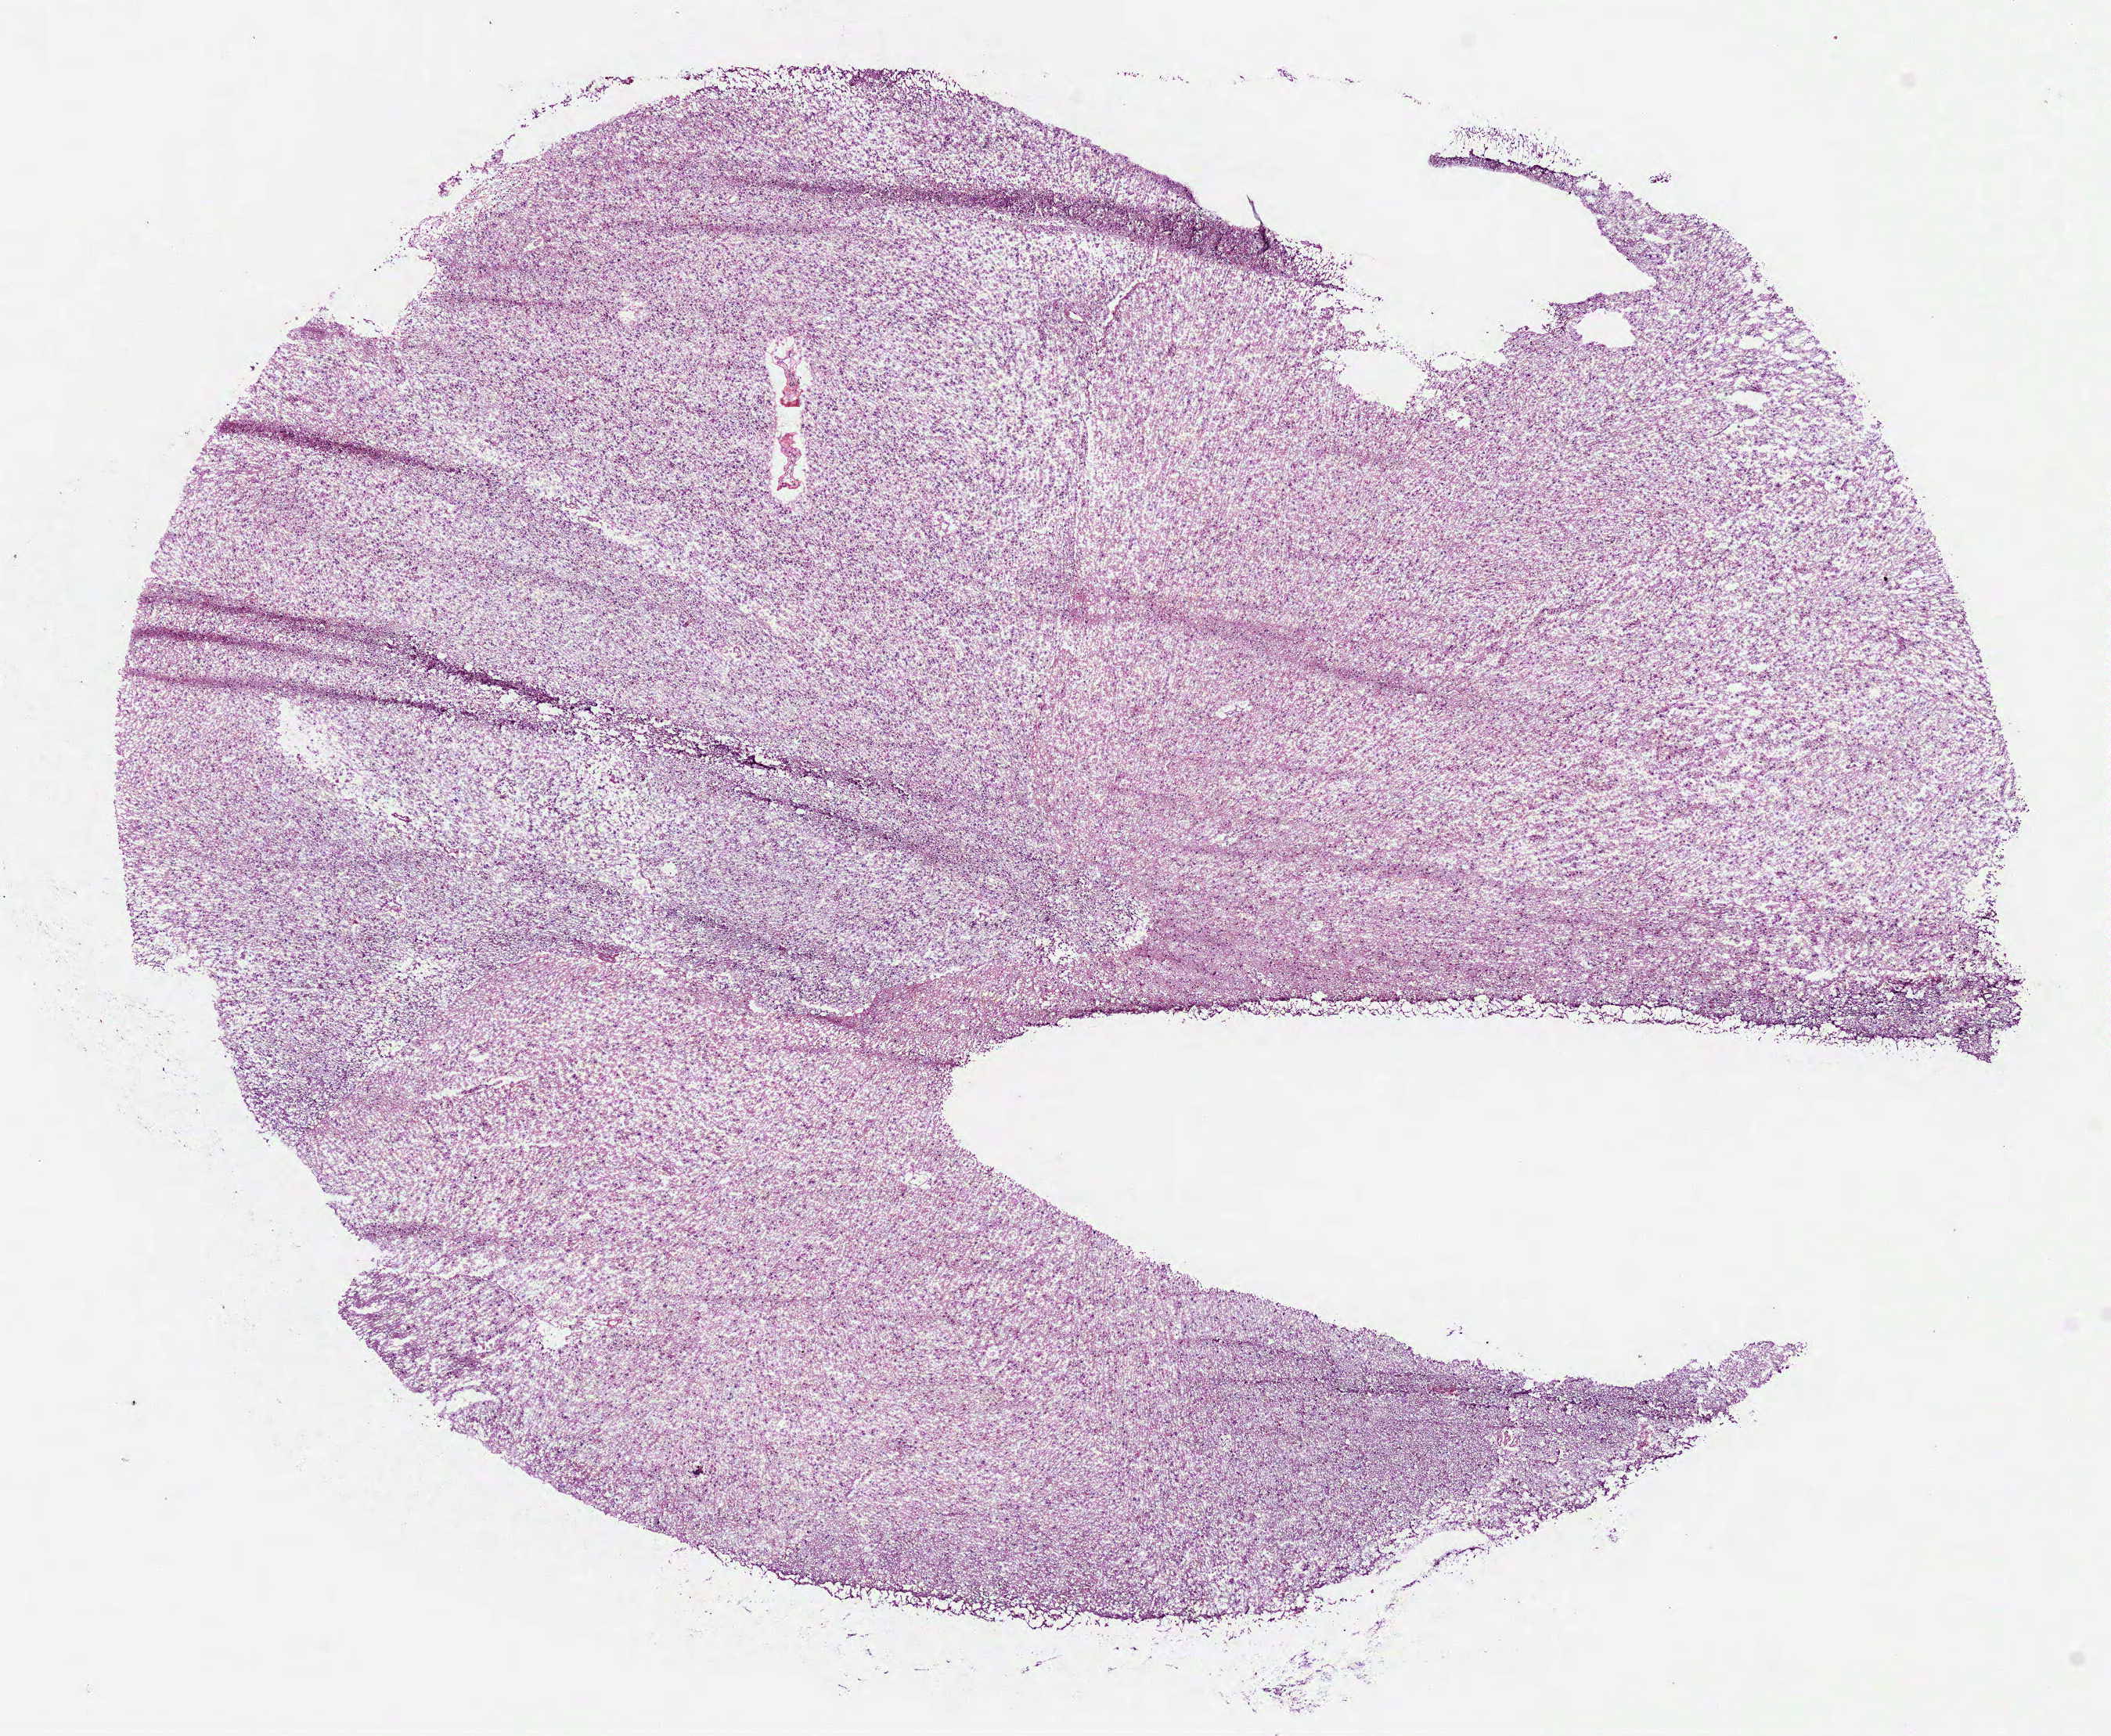
Whole-slide histology image, H&E, whole scanned area (about 10.9 x 8.9 mm) shown as a low-resolution overview. Frozen section. Primary tumour sample from the brain. Male patient; age at initial diagnosis 33 years. Histologic grade: G3 (poorly differentiated). Slide review estimates, as recorded: tumour cells 100%, tumour nuclei 70%, normal cells 0%, stromal cells 0%, necrosis 0%.
• pathologic diagnosis: Astrocytoma, anaplastic (cerebrum)
• laterality: left